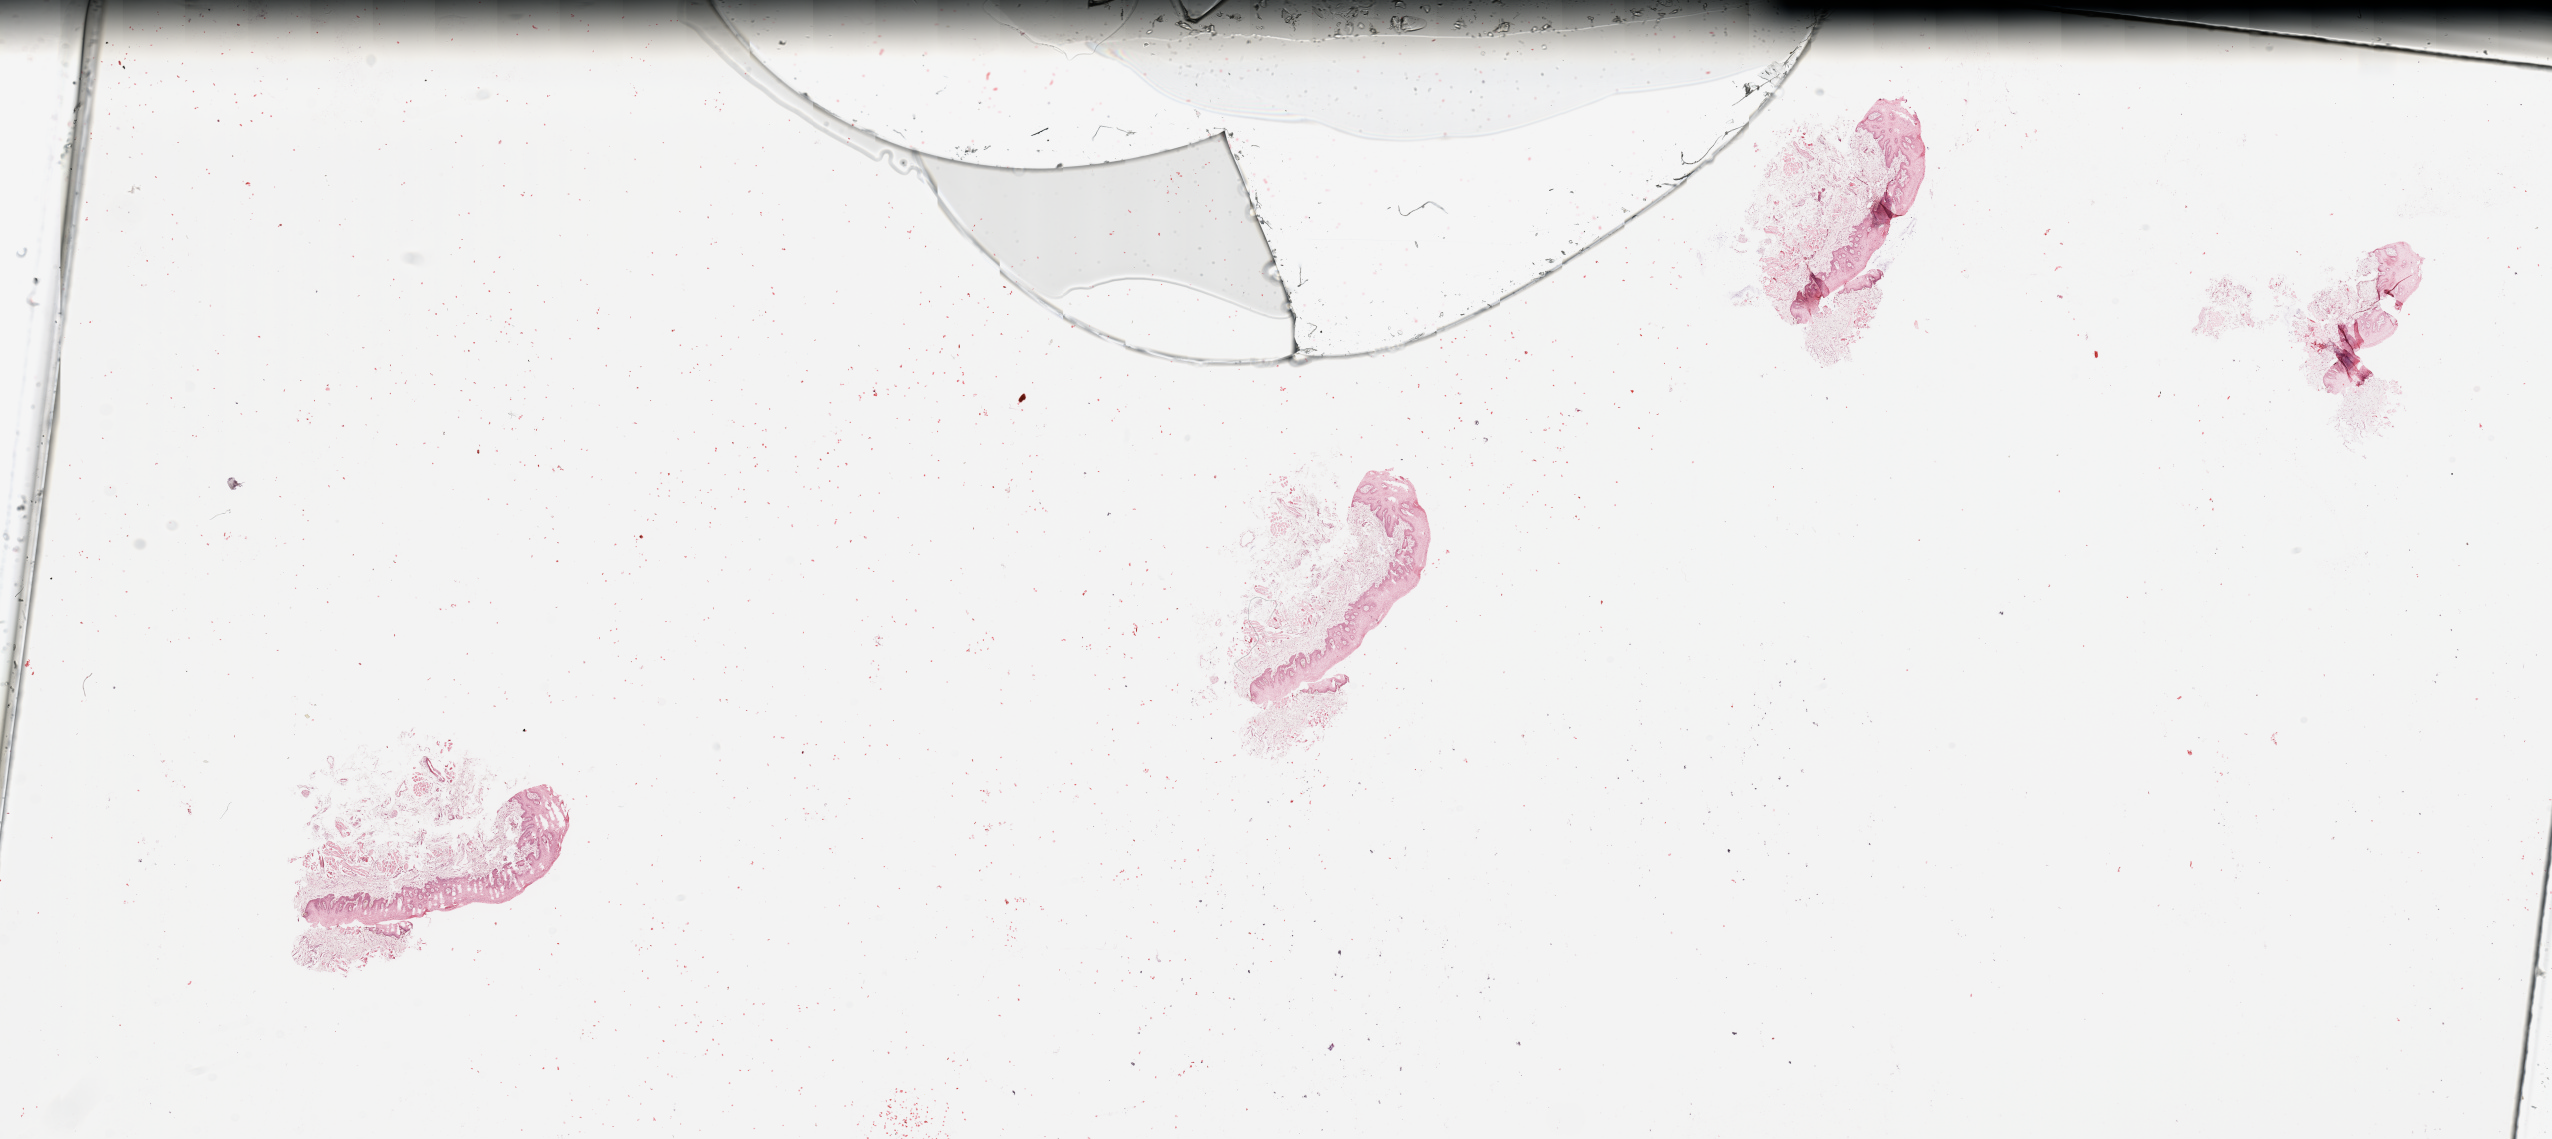
H&E-stained whole-slide image — shown as a low-resolution overview of the whole scanned area (about 40.4 x 18.0 mm, slide scanned at 20x); normal (non-tumour) tissue sample, sampled site: floor of mouth. Male, 49 y/o.
* this section: normal (non-tumour) tissue from the same patient
* patient diagnosis: Squamous cell carcinoma, NOS (floor of mouth, NOS)